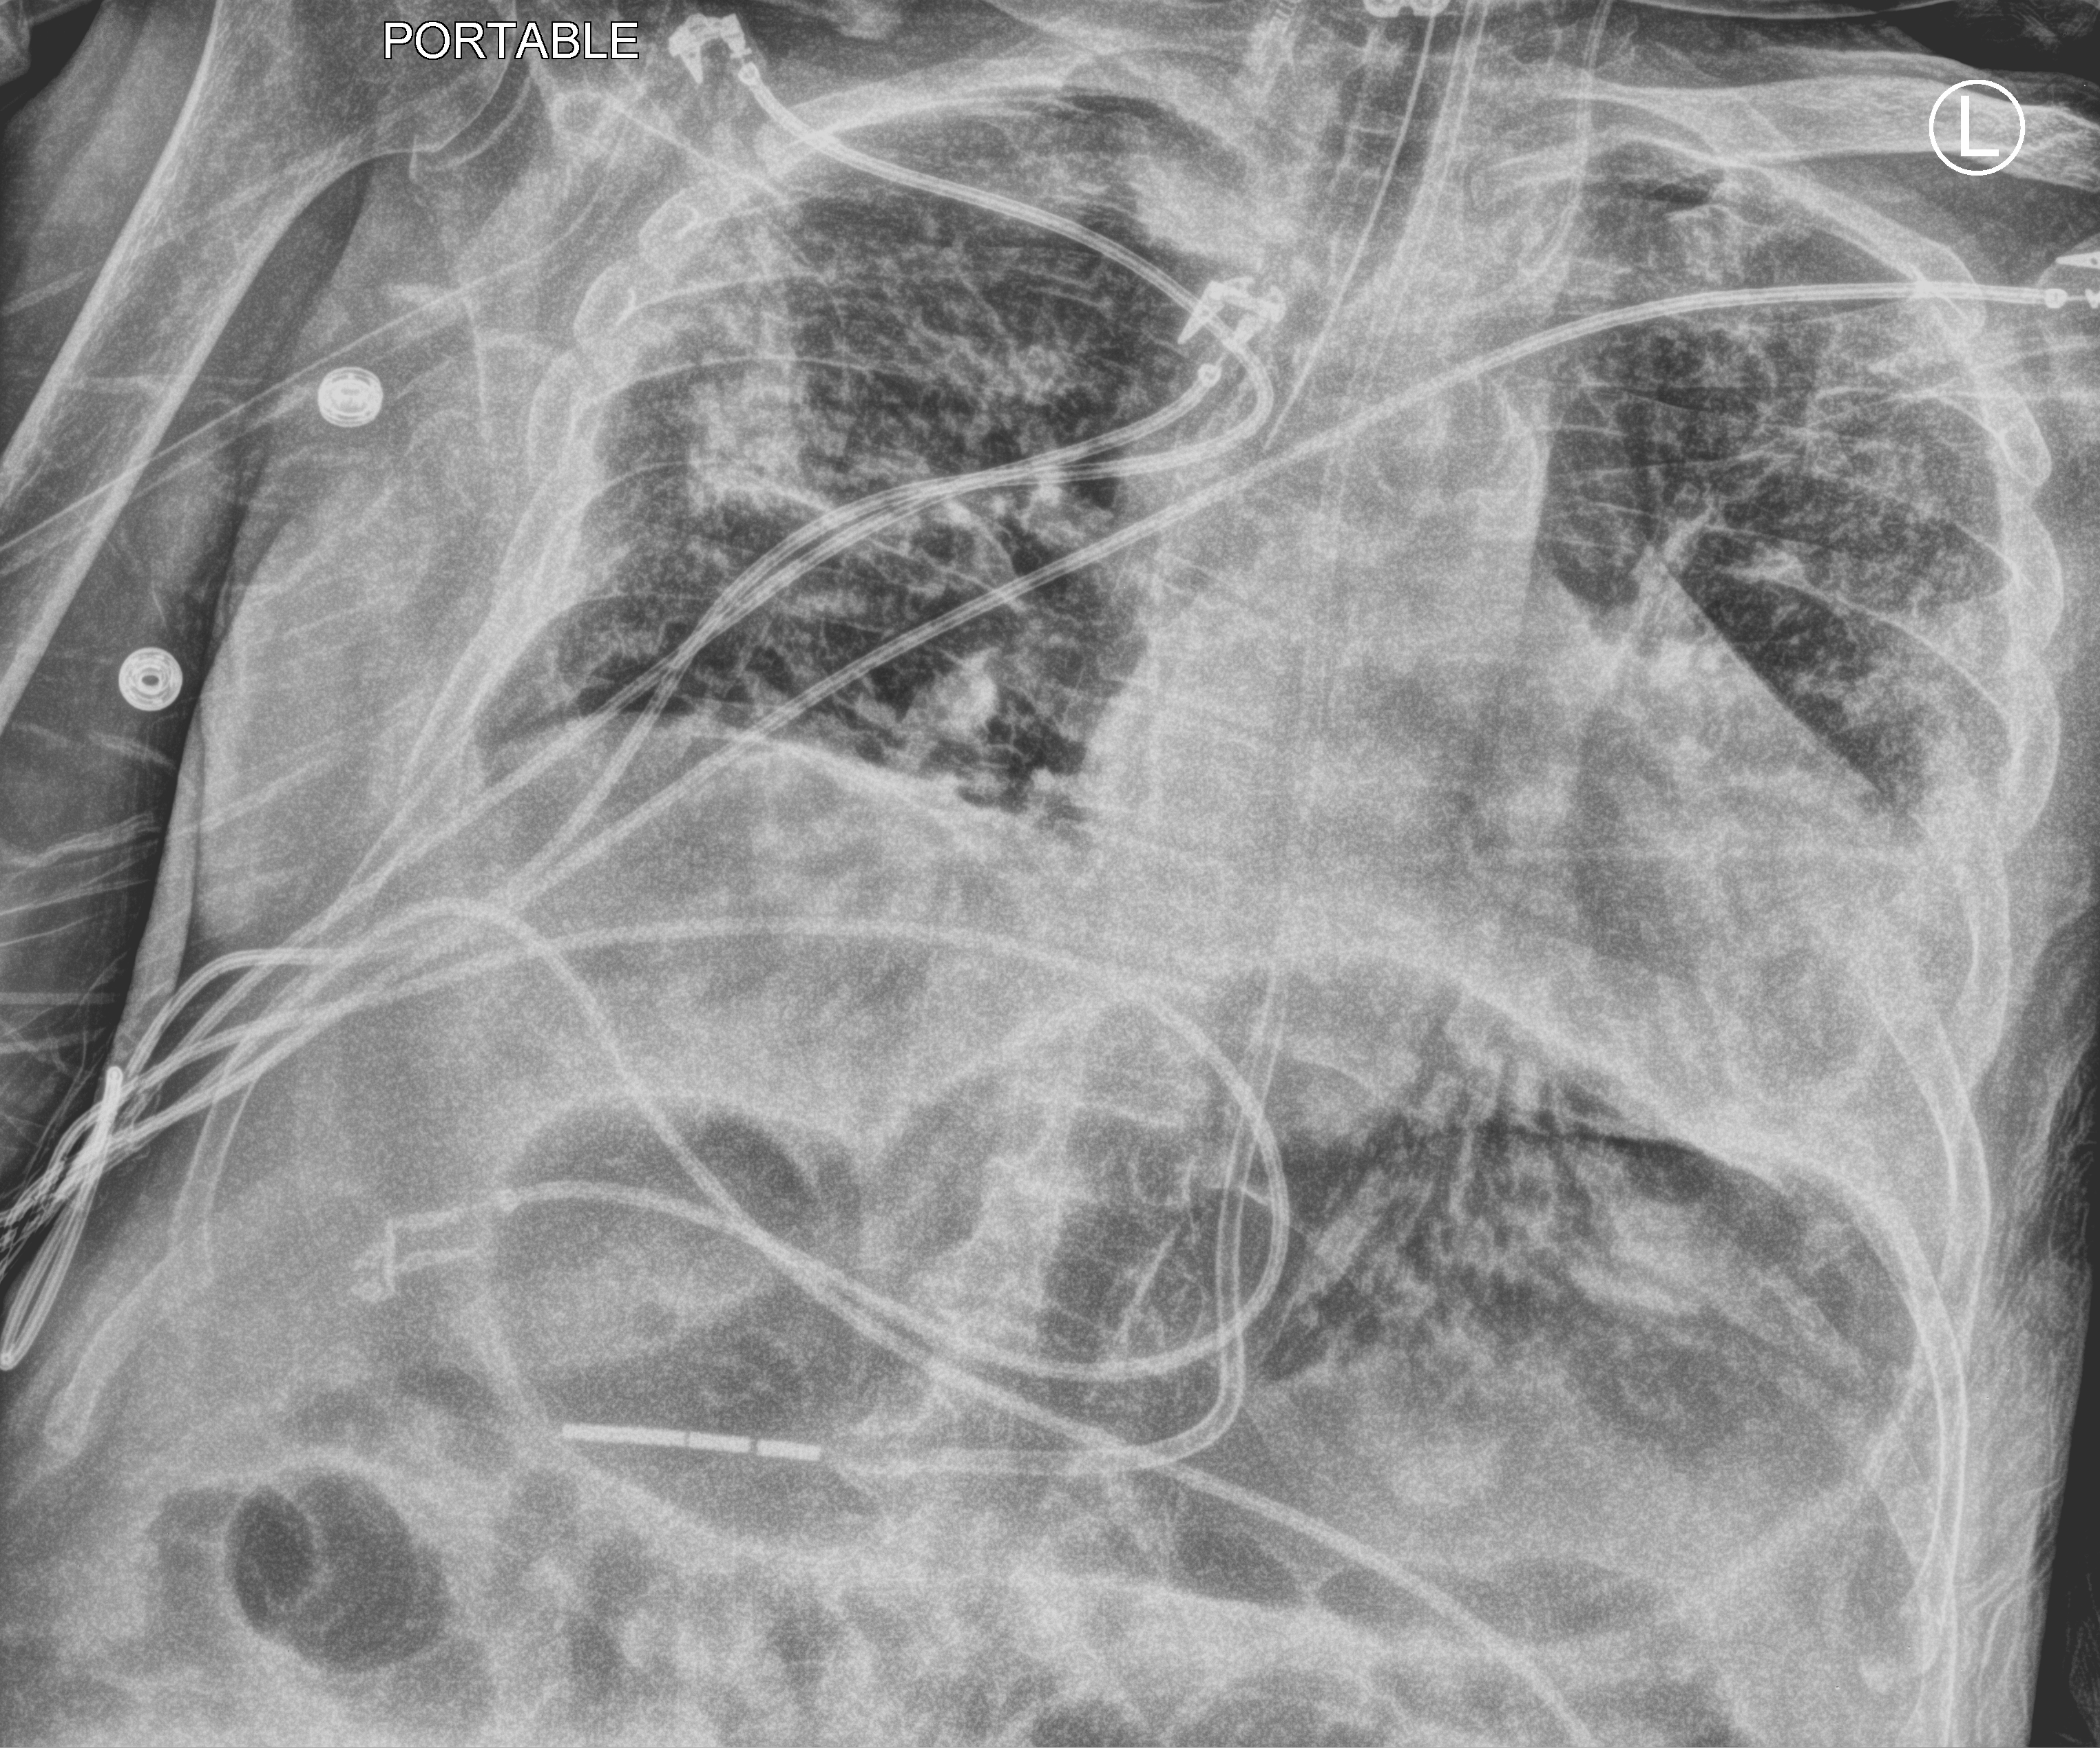
Bedside chest radiograph (computed radiography), anteroposterior (AP) projection. Male patient hospitalised with COVID-19, age 75–90 years.
Hospital-stay facts (about this admission, not read from this image; timing relative to this image not recorded):
- smoking status (admission record): former
- COPD (admission record): no